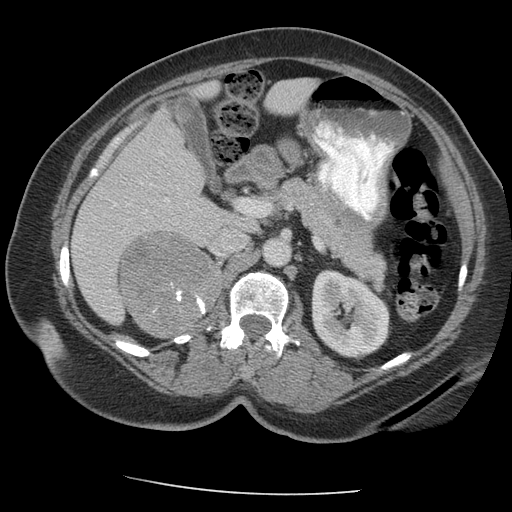
Contrast-enhanced abdominal CT, one axial slice. Position 120 of 163 along the scan axis. Intravenous contrast given. Soft-tissue window (W 400 / L 40 HU). 2.5 mm slice thickness. 512 × 512 image matrix, field of view 360 × 360 mm. Patient: female, 70 years. Case-level facts recorded for this patient, not image findings: diagnosis: adrenocortical carcinoma; tumour side: right adrenal; tumour size at pathology: 9.5 cm.
Outlined on this slice (semi-automatic segmentation, software-assisted and operator-edited):
- mass: bounding box <120,233,221,337> (left, top, right, bottom; pixels)